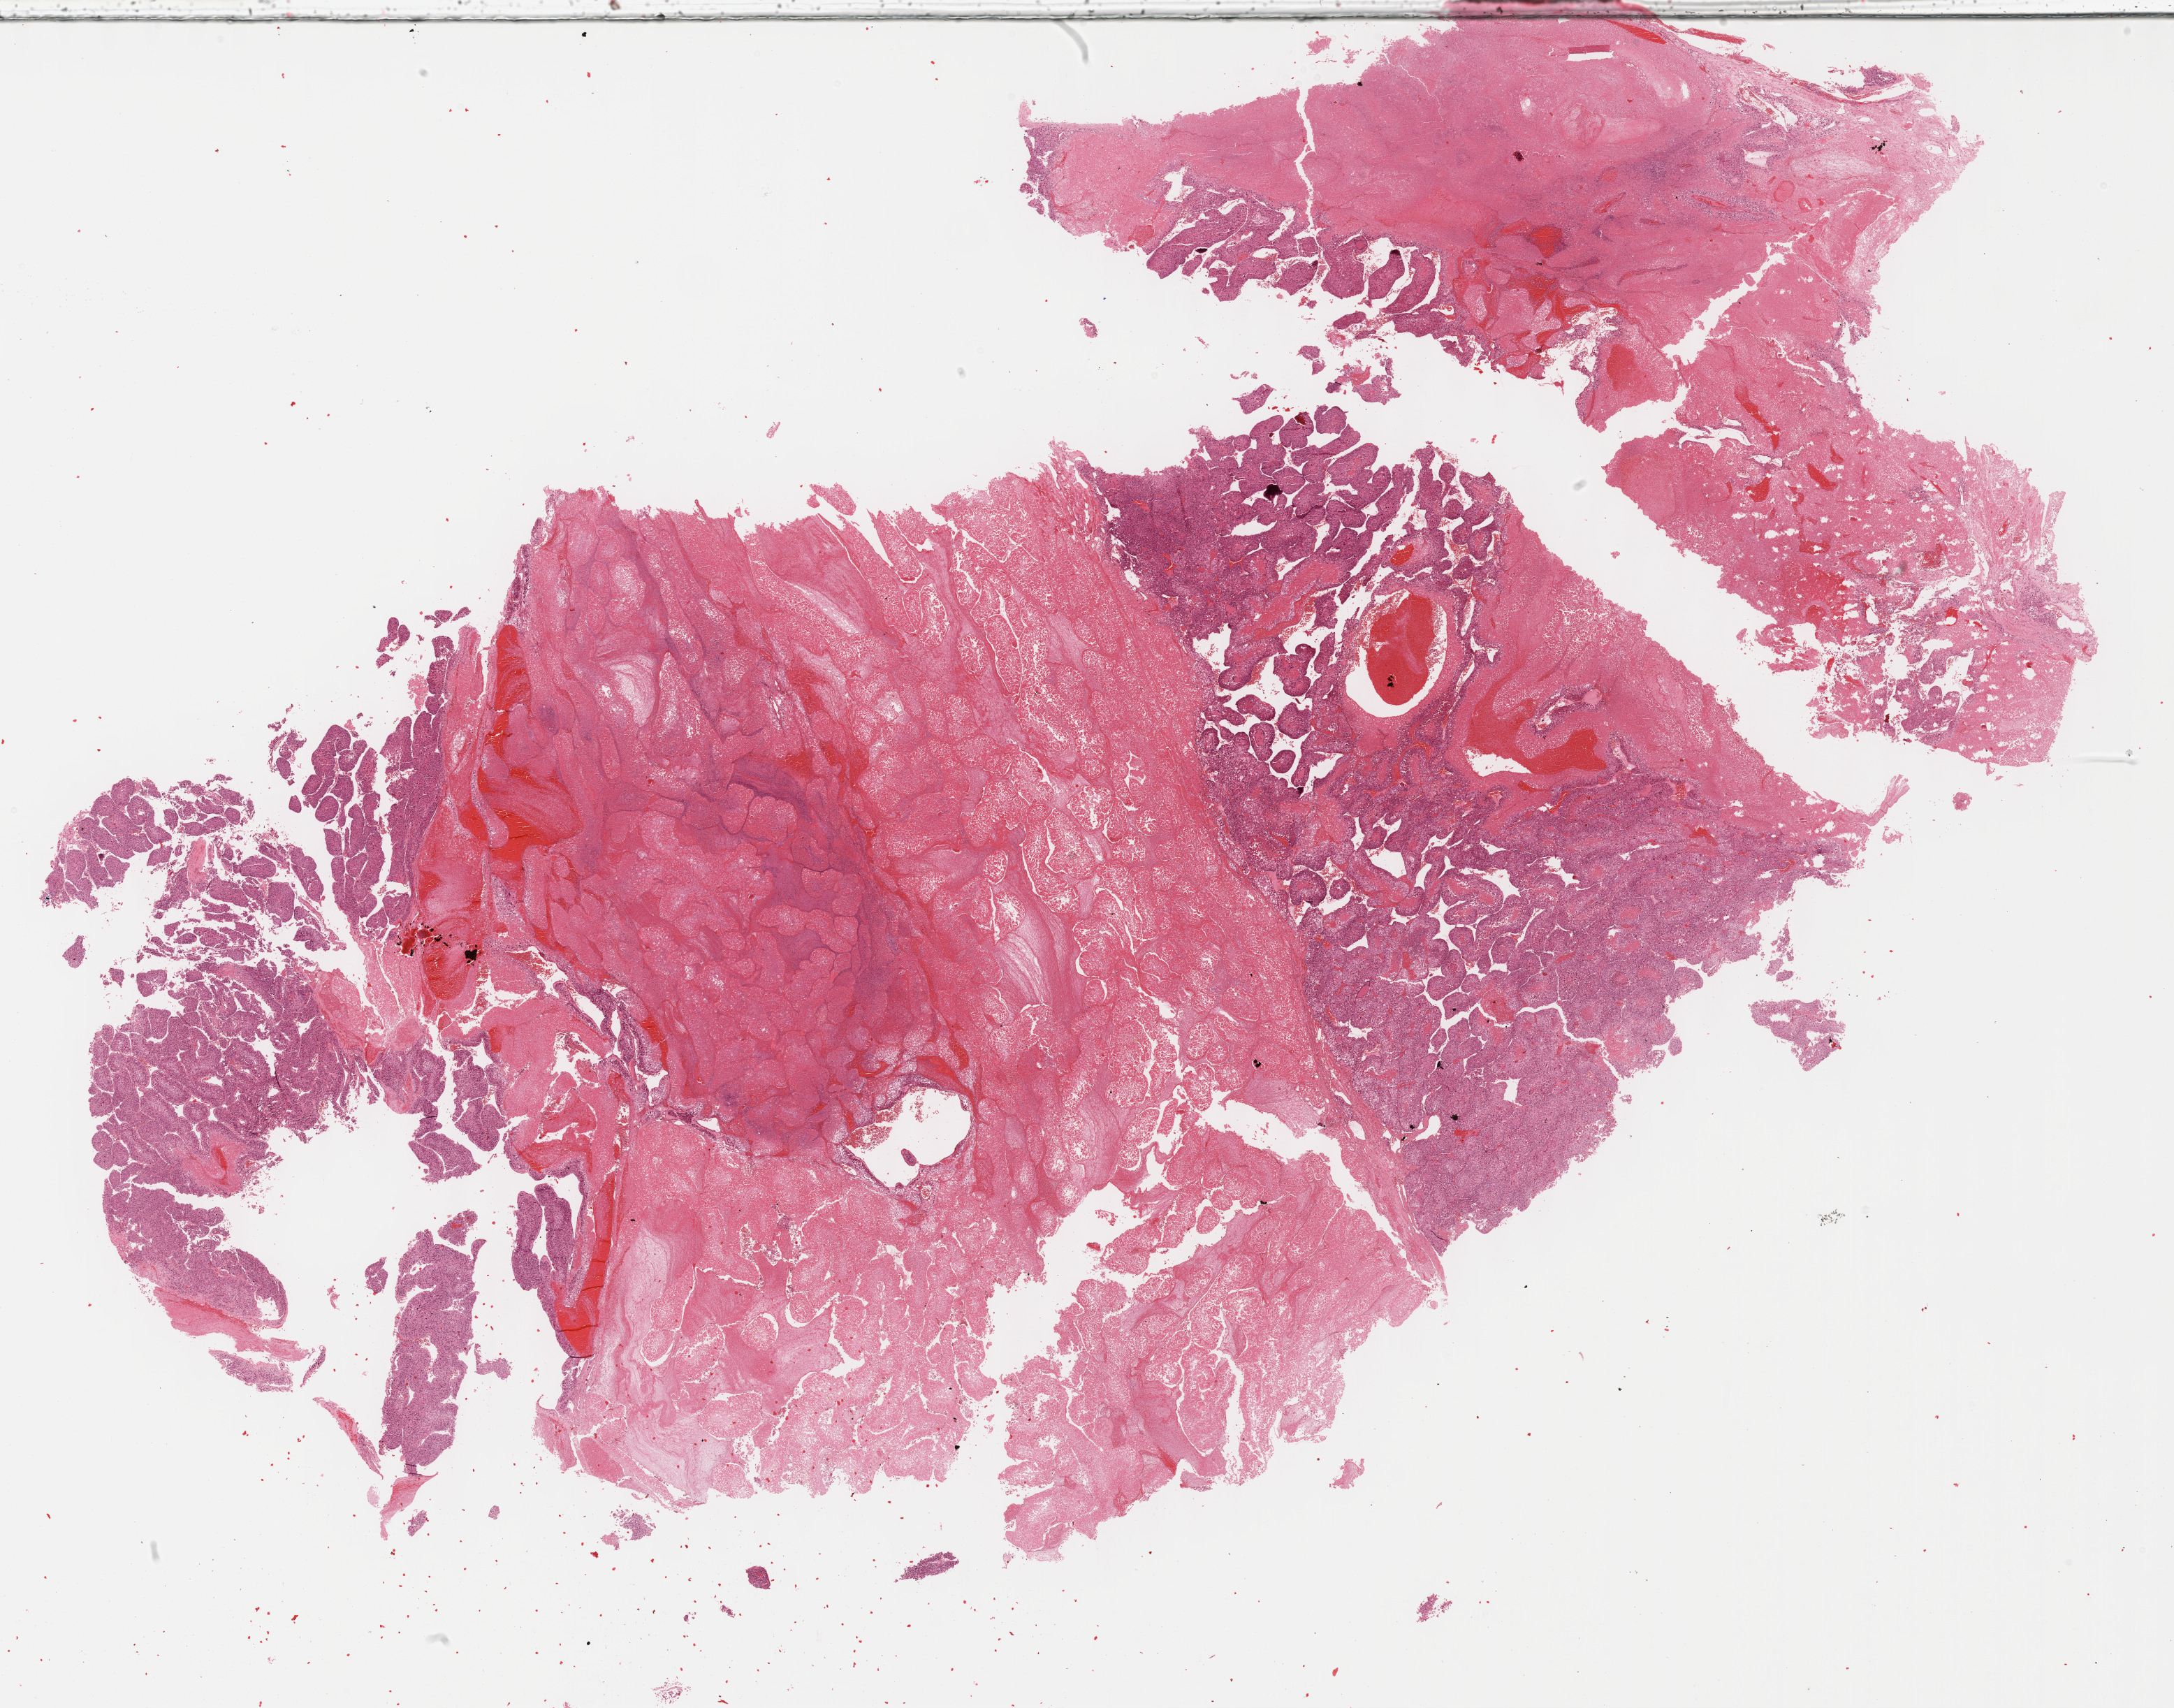
Whole-slide histology image, H&E — a low-resolution overview of the entire scanned area, about 25.1 x 19.8 mm, FFPE section, adrenal cortex, primary tumour sample. Female patient; age at initial diagnosis 53 years.
* histologic diagnosis: Adrenal cortical carcinoma
* laterality: right